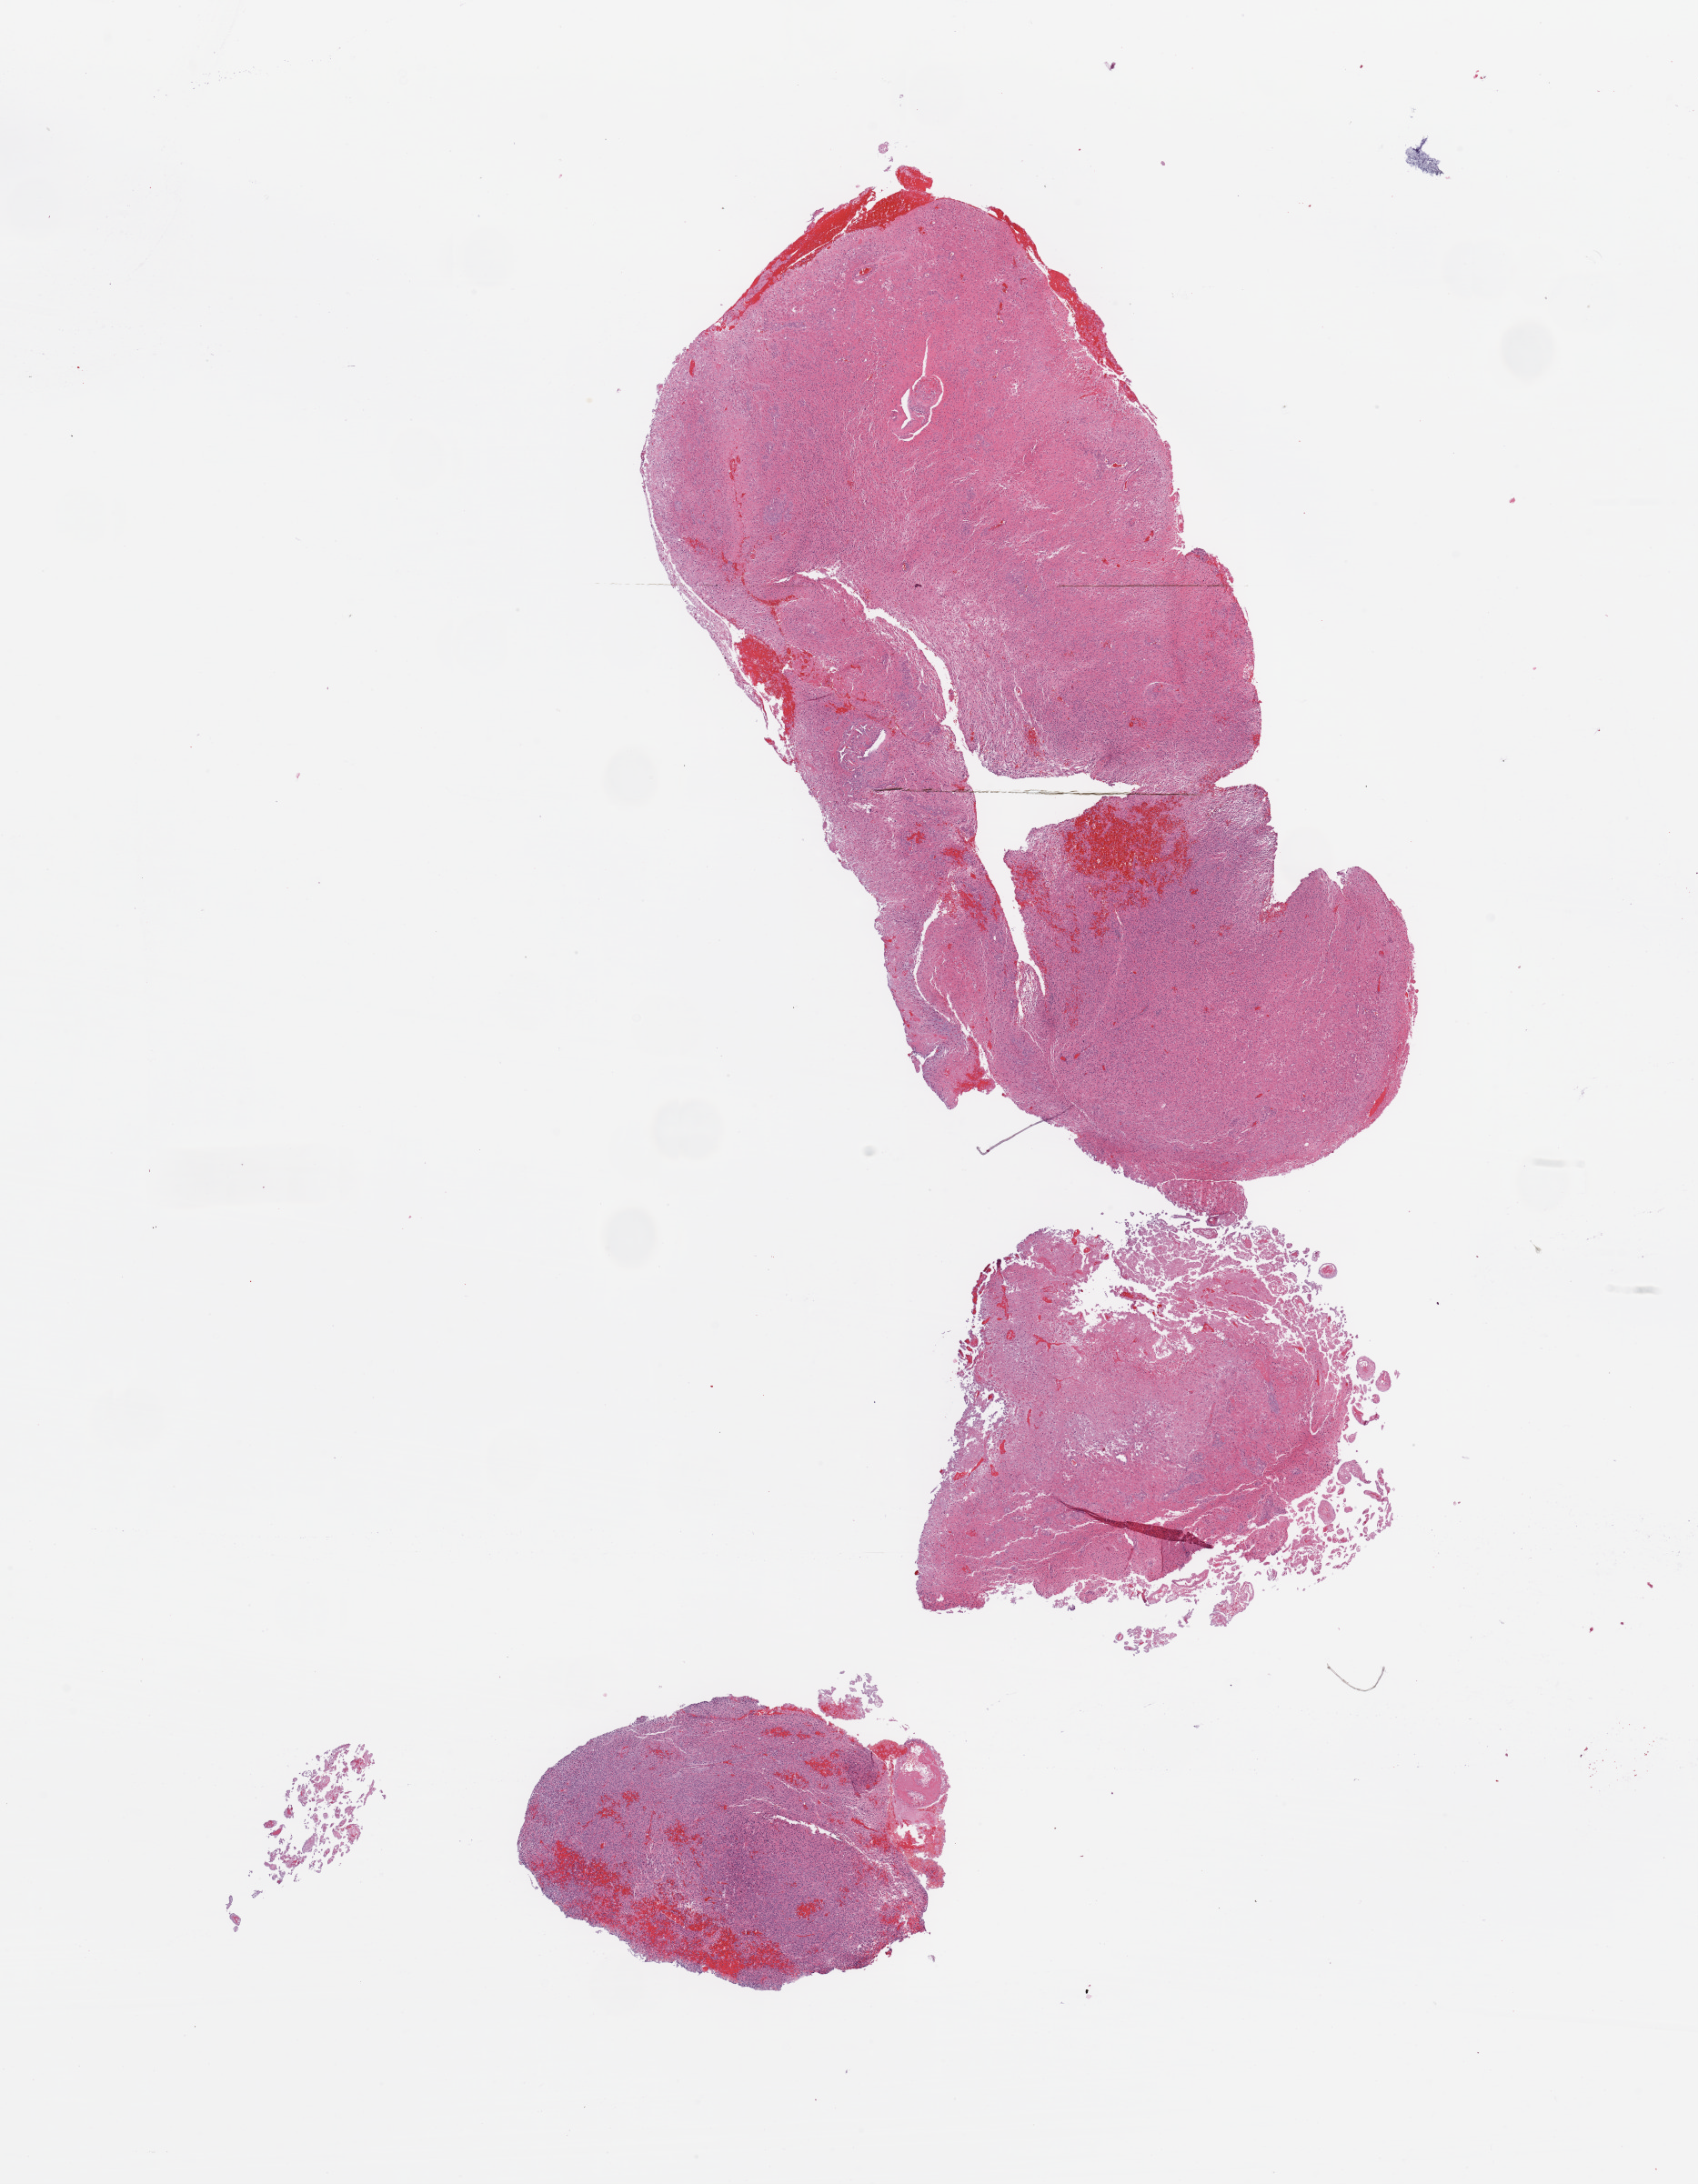
H&E whole-slide image, shown as a low-resolution overview of the whole scanned area (about 14.8 x 19.0 mm, slide scanned at 20x). Tumour tissue sample, sampled site: frontal lobe. Male, 54 y/o. Composition of this section per pathologist review: tumour nuclei 80%, necrosis 5%.
Histologic diagnosis: Glioblastoma. Primary tumour site (as recorded): frontal lobe.